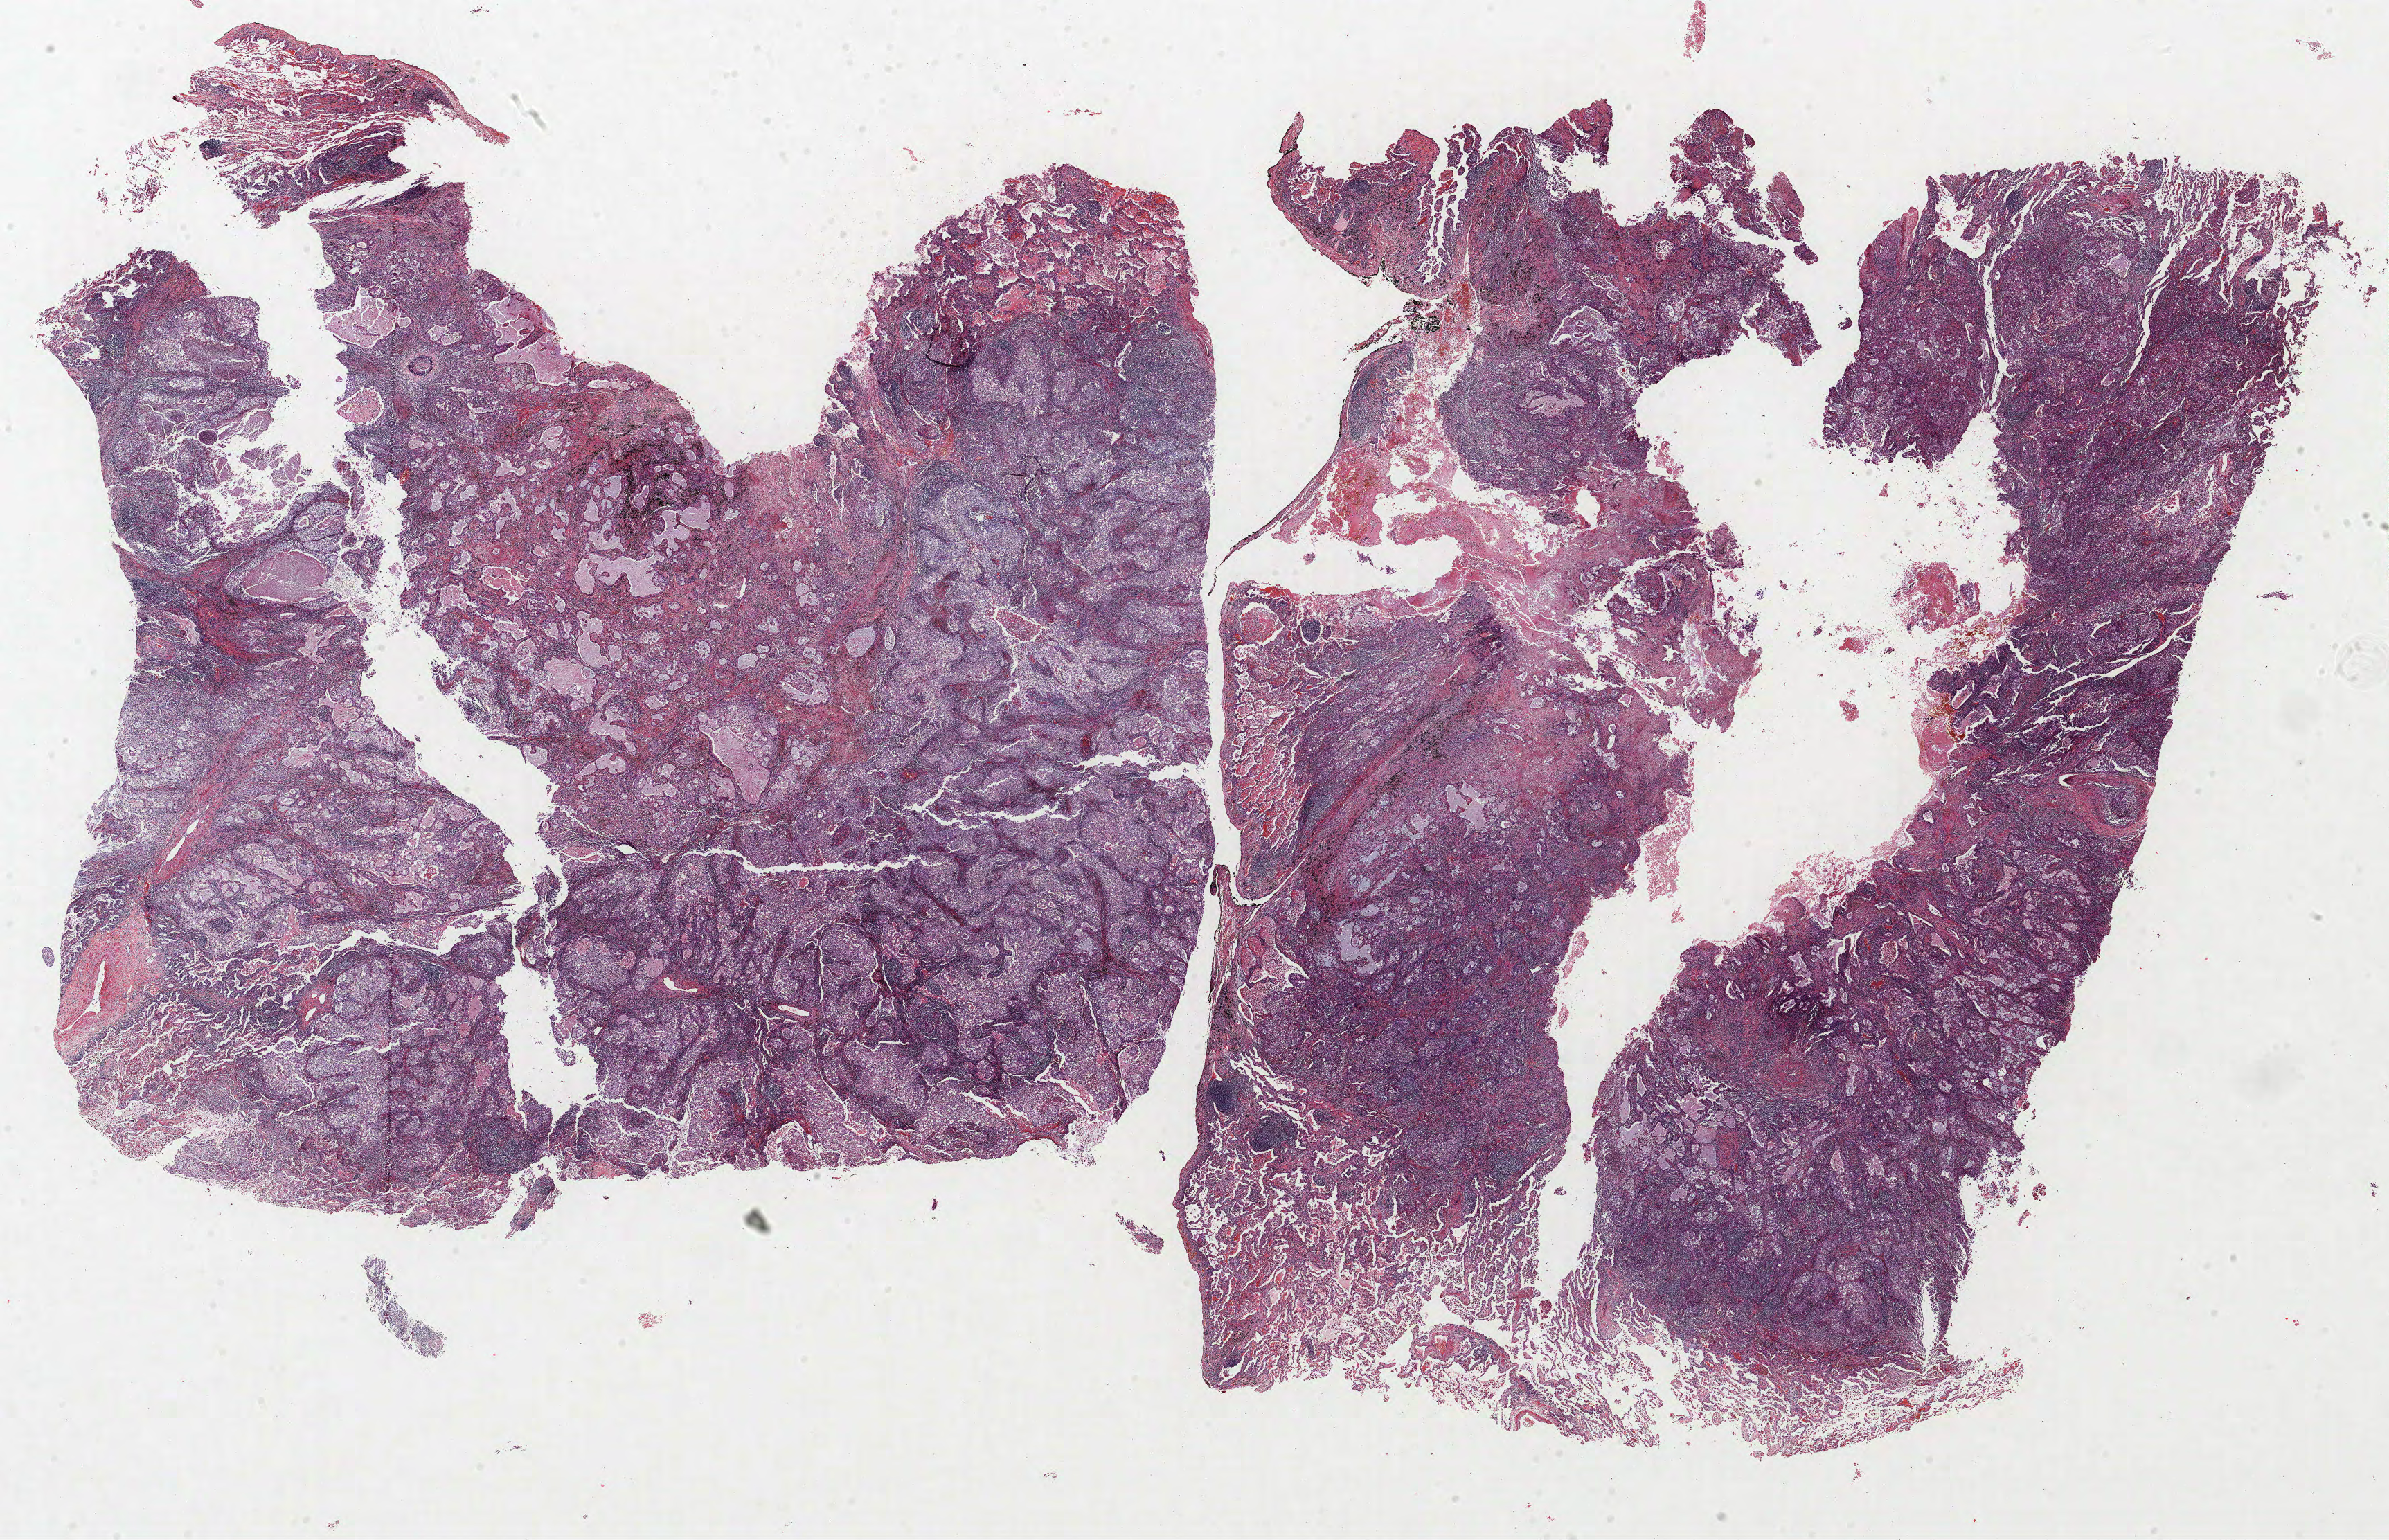
H&E-stained whole-slide image — low-resolution overview of the scanned area, about 27.6 x 17.8 mm (slide scanned at 40x); FFPE section; lung tissue. Male, age 71 at enrolment. Current smoker at enrolment. Grade: poorly differentiated (G3).
* participant's lung-cancer diagnosis: Adenocarcinoma, NOS
* tumour size (pathology): 25 mm
* primary tumour location (clinical record): left upper lobe
* stage (AJCC 6th edition): IIIB